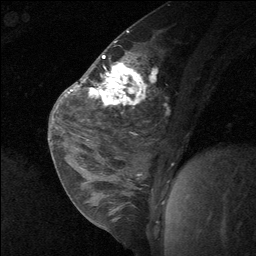
Breast MRI (dynamic contrast-enhanced), one sagittal slice. Slice 35 of 64 in the series (ordered by position). Dynamic contrast-enhanced study with each time point stored as its own series, time point 2 of 3 at this slice position (early post-contrast, ordered by acquisition time). 1.5 T. TE 4.8 ms, TR 27 ms. 256 × 256 image matrix, field of view 180 × 180 mm. Female patient, age 26 years. From the clinical record (not read from this slice): setting: breast cancer imaged before/during neoadjuvant chemotherapy; receptor status: HR-positive, HER2-negative.
Outlined on this slice (semi-automatic segmentation, software-assisted and operator-edited):
- analysis volume of interest (the breast-tissue region the enhancement analysis was run in; not a lesion): bounding box [x1, y1, x2, y2] px = [86, 43, 142, 138]
- tumour enhancement mask (voxels above the 90 % enhancement threshold inside the analysis volume of interest): [89, 62, 136, 104]